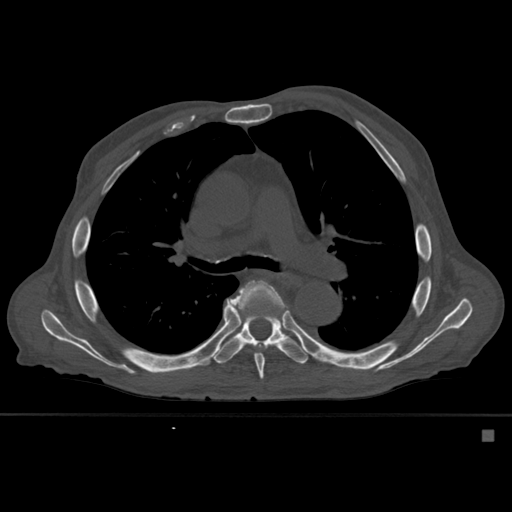
CT including the spine, one axial slice. Slice 376 of 527 in the series (ordered by position). Bone window (W 1800 / L 400 HU). 1.5 mm slice thickness. 512 × 512 image matrix. Patient: male, 78 years. From the clinical record (not read from this slice): primary cancer: prostate.
Annotated regions visible in this slice (semi-automatic segmentation, software-assisted and operator-edited):
- T6 vertebra: bounding box [x1, y1, x2, y2] px = [228, 280, 288, 380]
- T7 vertebra: [213, 297, 309, 364]